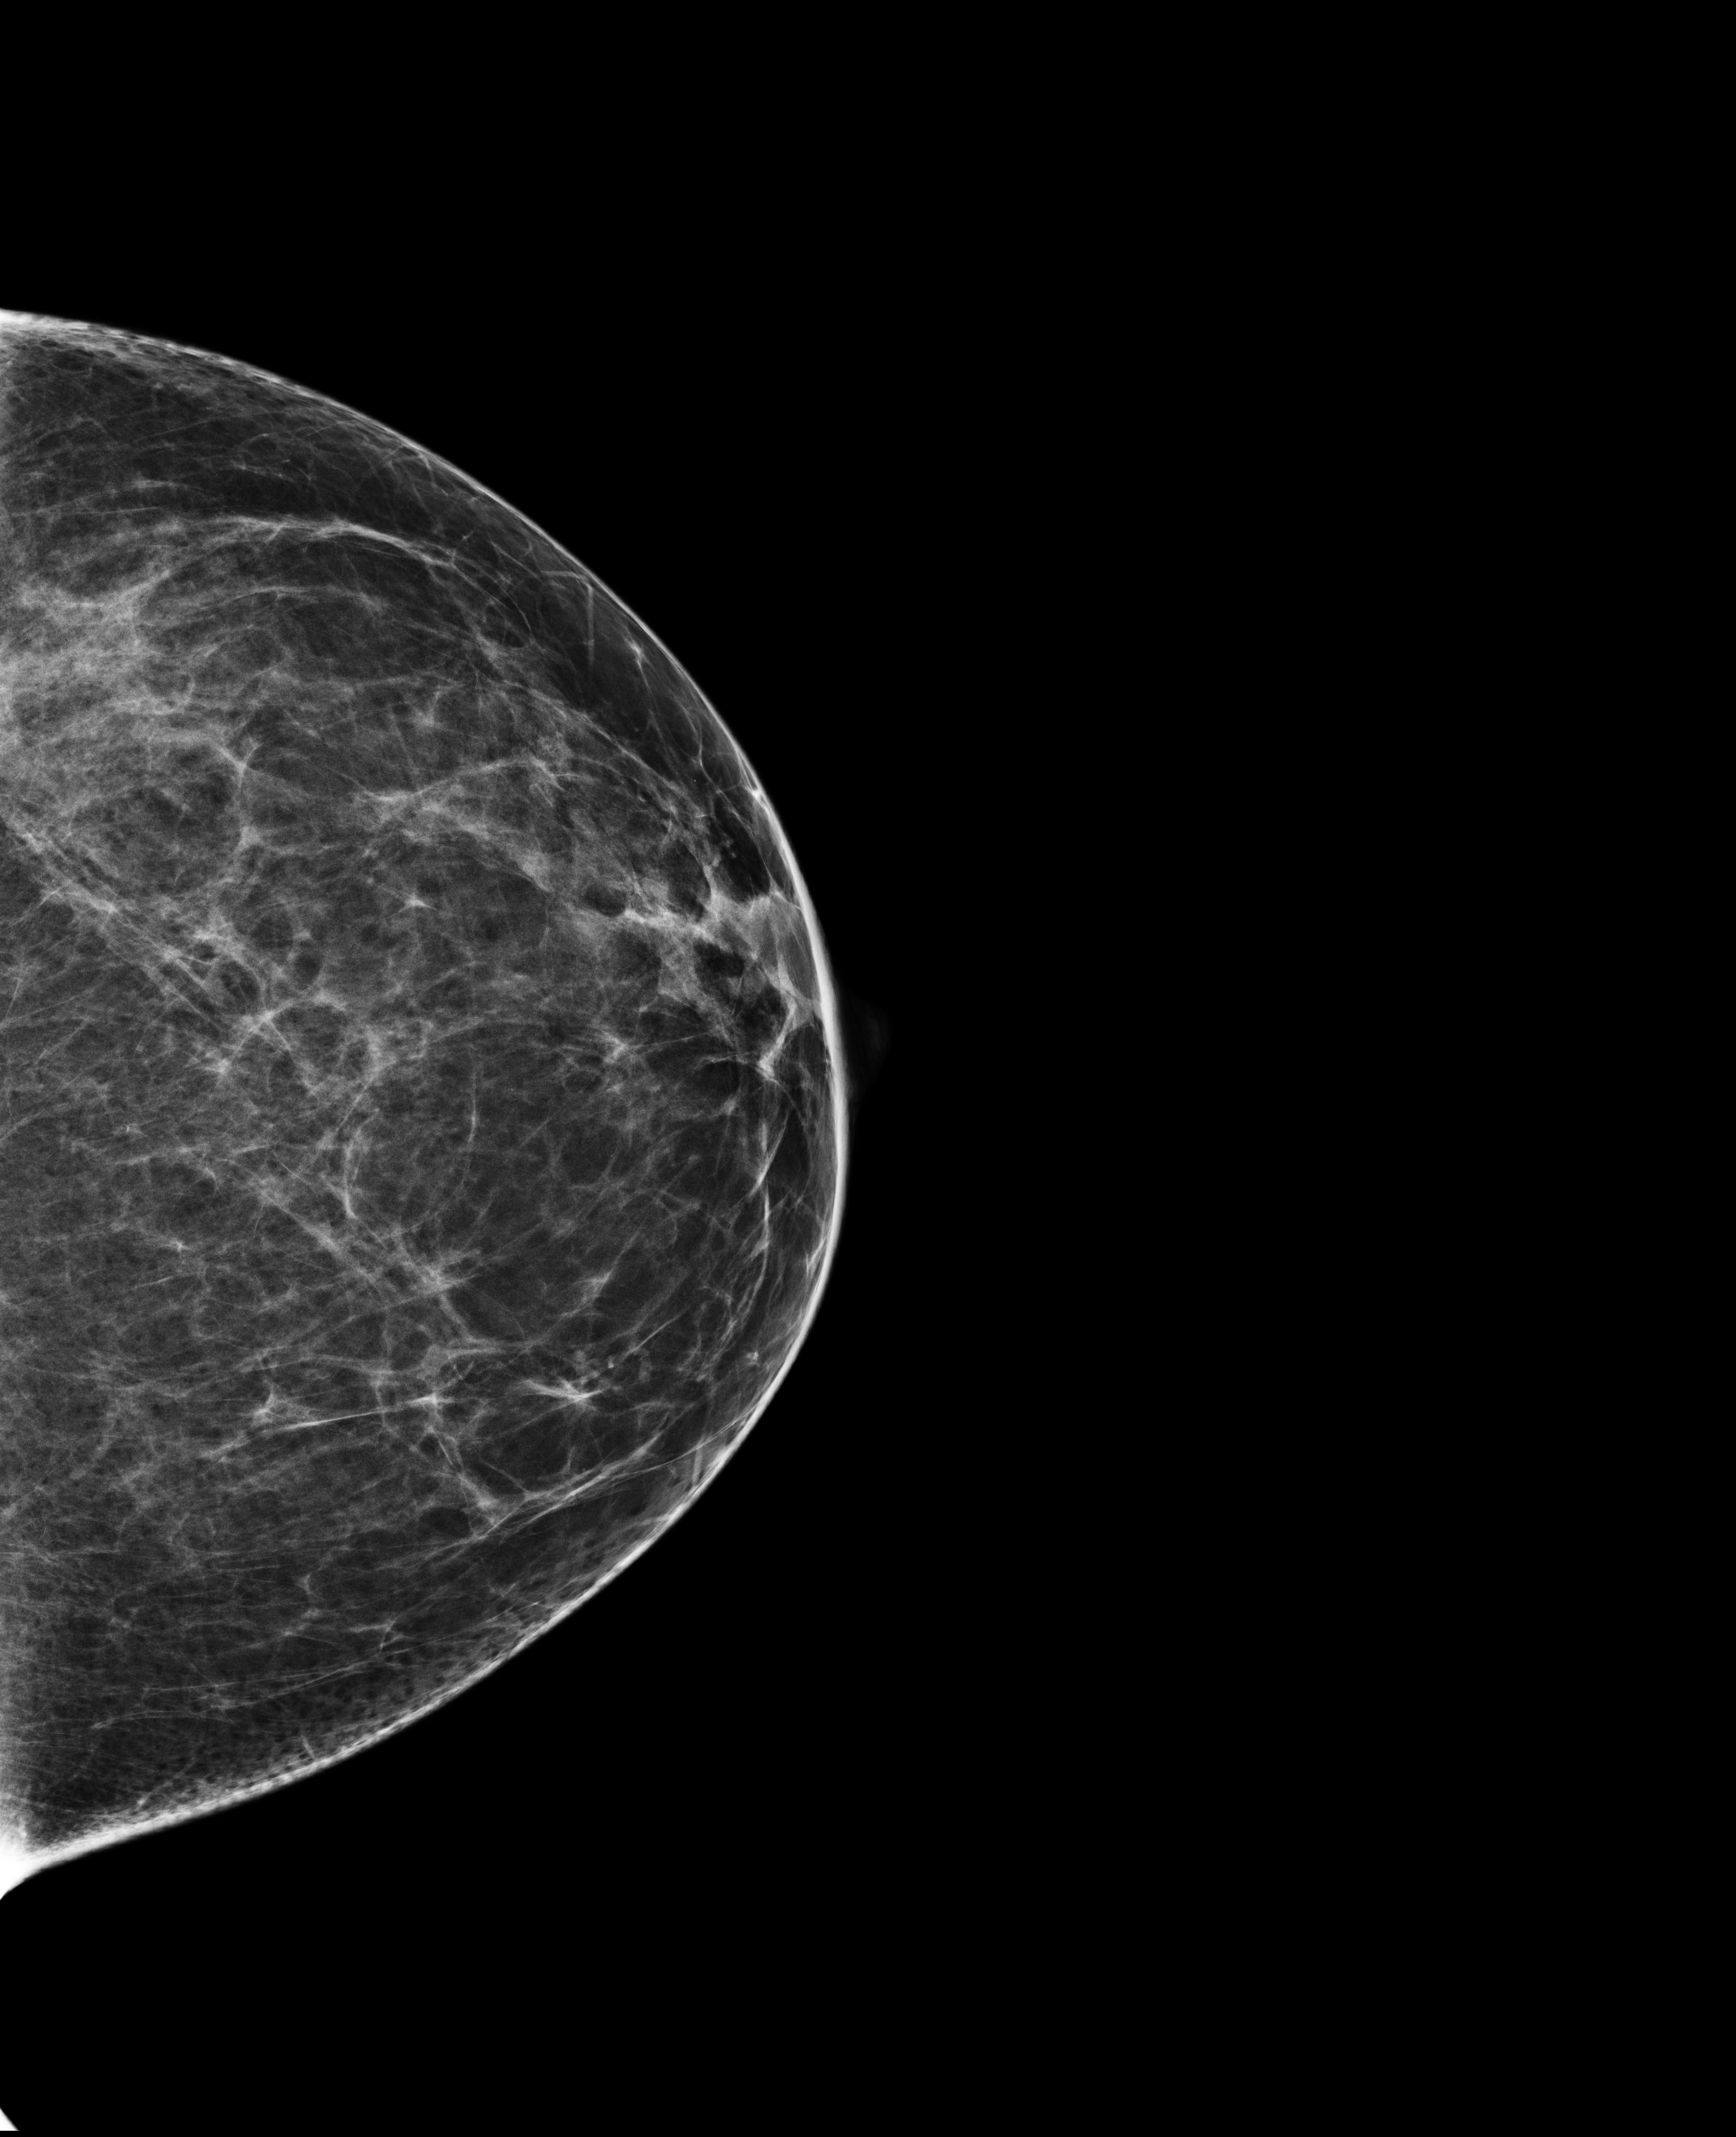
Screening examination, system: Selenia Dimensions. Patient aged 42 years (female).
Image type: full-field digital mammogram. Breast: left. Projection: cranio-caudal projection.